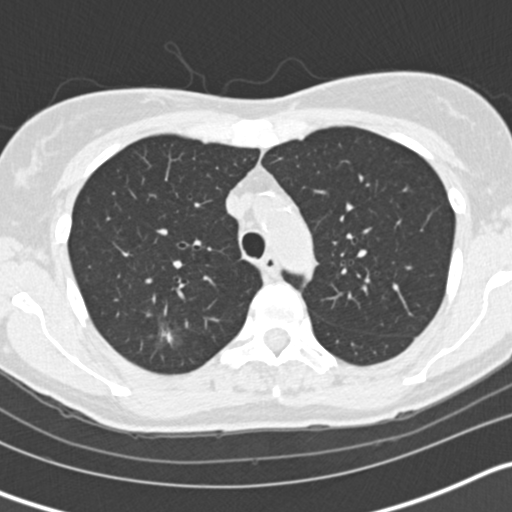
Low-dose screening chest CT, one axial slice. Slice 118 of 163 in the series (ordered by position). Reconstruction kernel B30f. 120 kVp. Lung window (W 1500 / L -600 HU). 512 × 512 image matrix.
Outlined on this slice (outlined manually by an expert reader):
- lesion 1 (tumor, upper lobe of right lung): bounding box (x1, y1, x2, y2) in pixels: (161, 330, 173, 344)